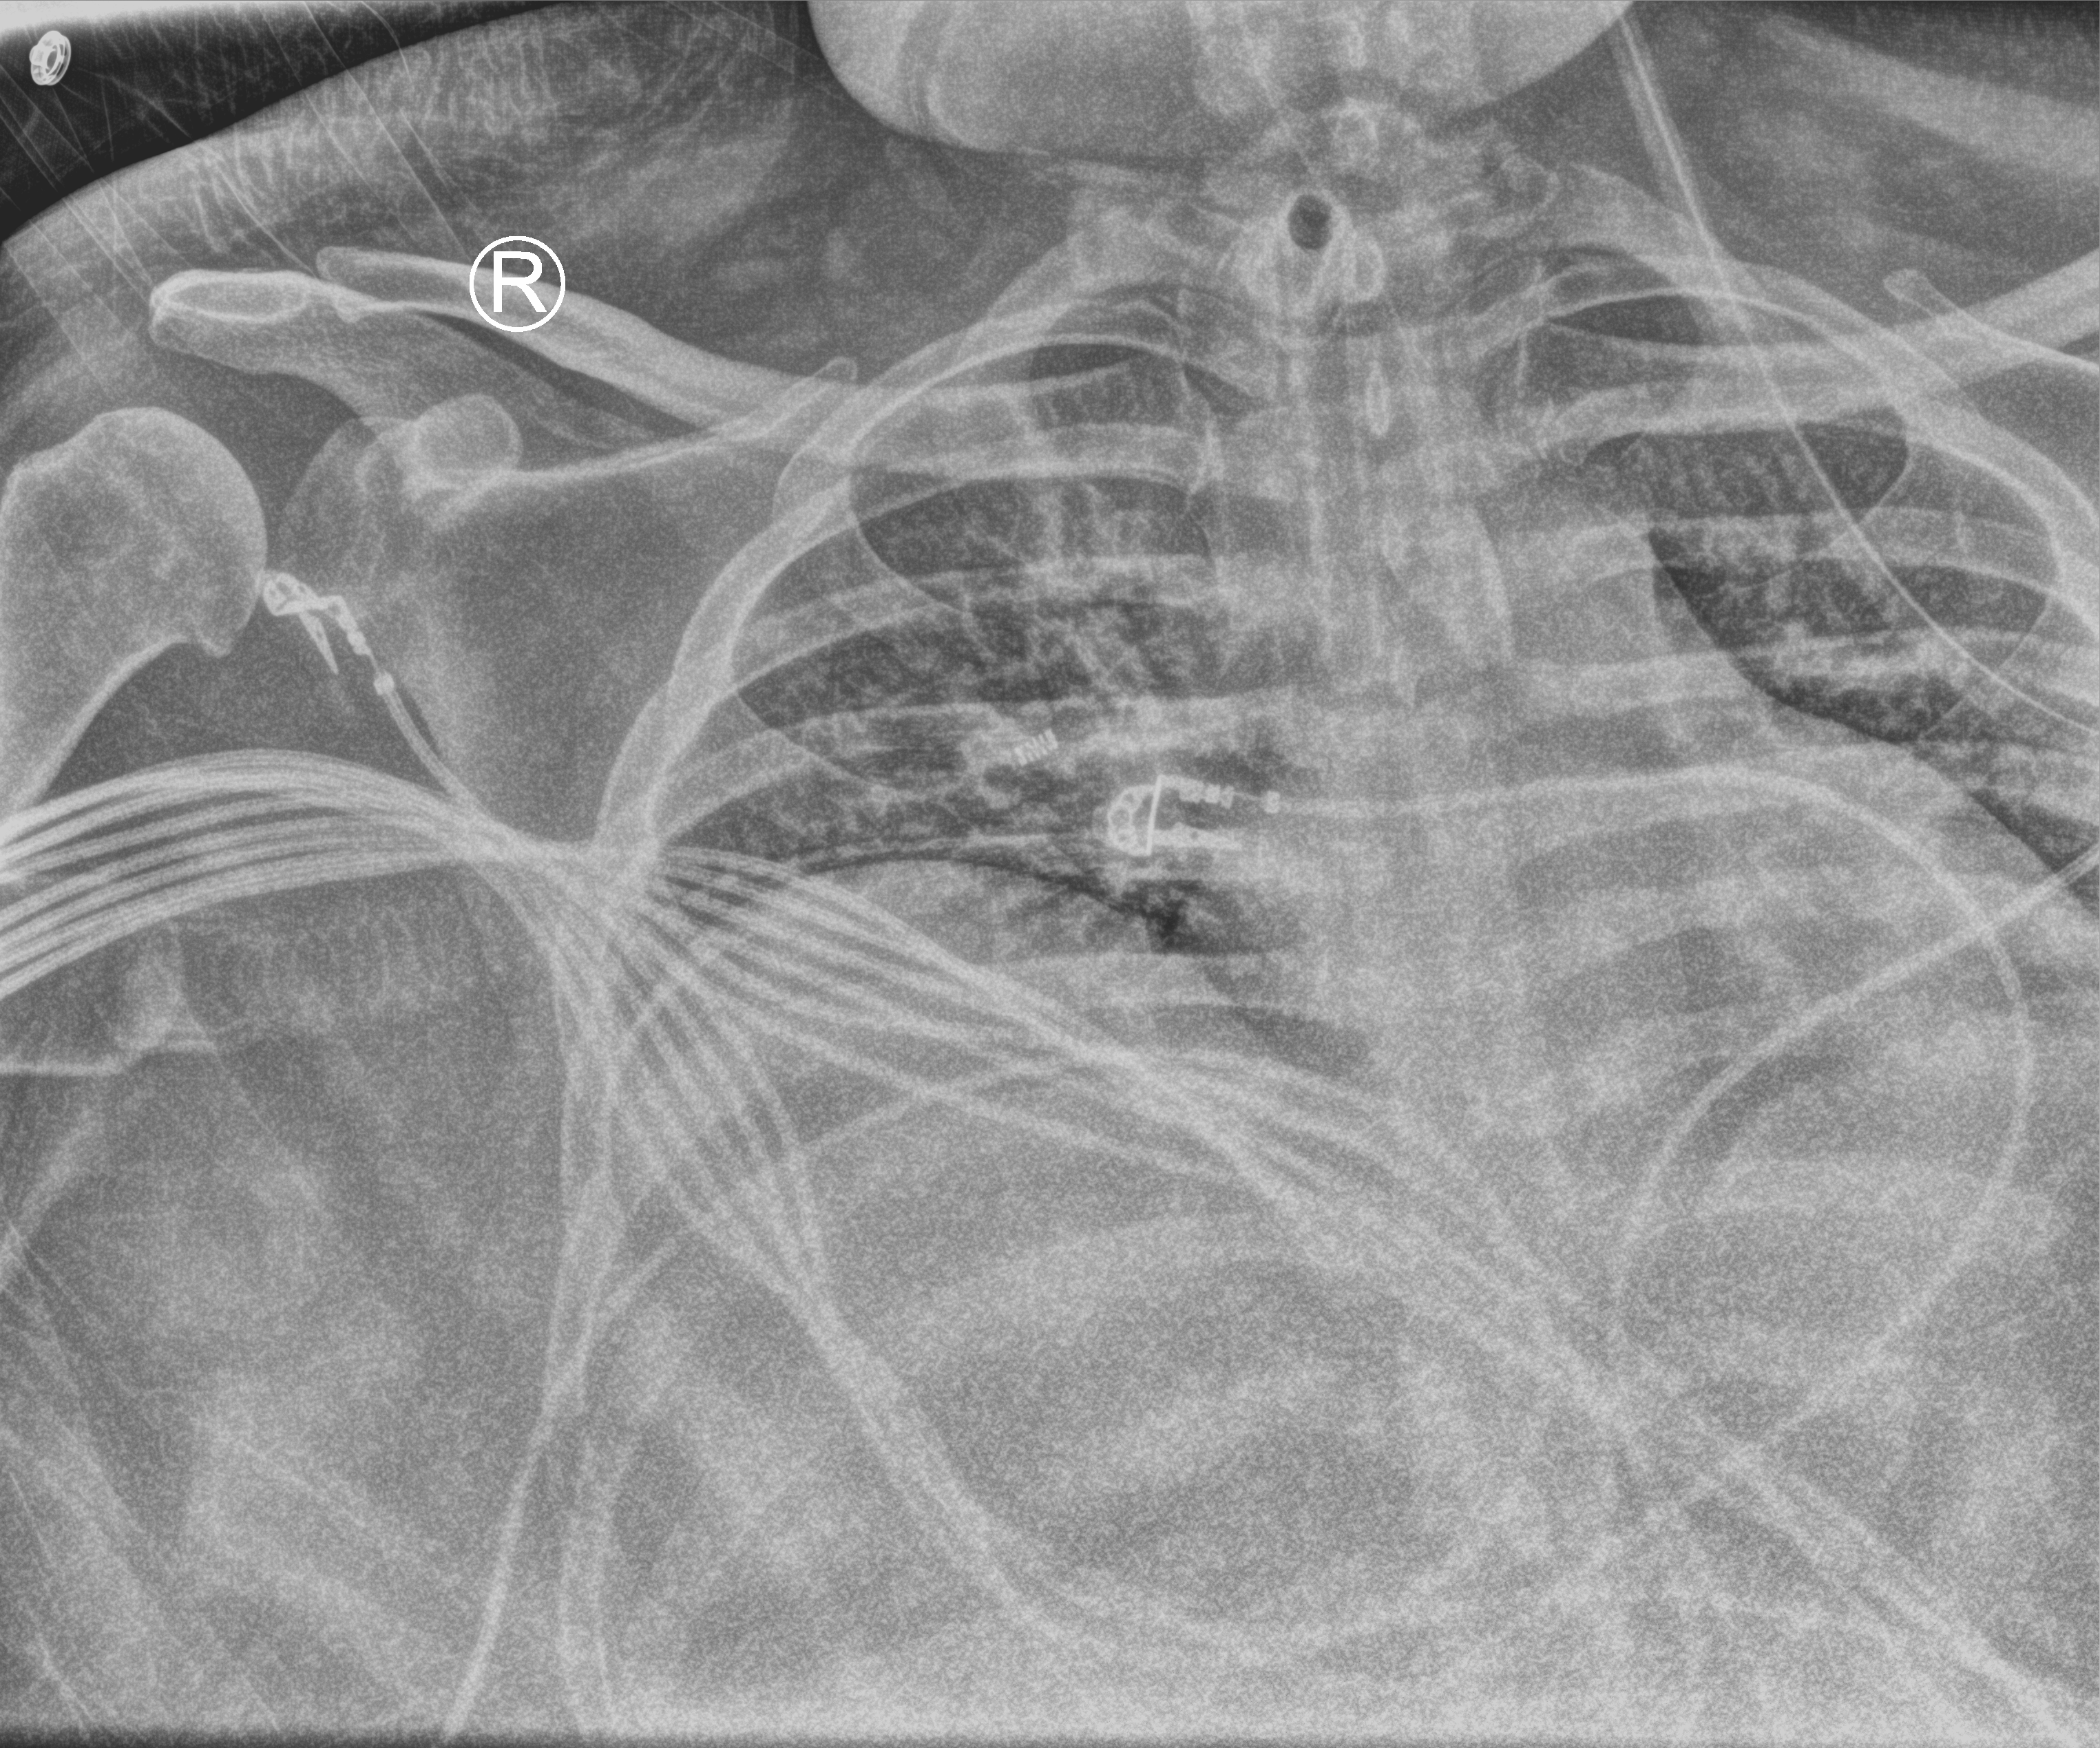
Bedside chest radiograph (computed radiography); anteroposterior (AP) projection. Male patient hospitalised with COVID-19, age 18–59 years.
Hospital-stay facts (about this admission, not read from this image; timing relative to this image not recorded): hypertension (admission record): no; admitted to intensive care during this hospital stay: yes.